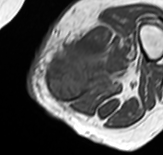
MRI of an extremity soft-tissue mass, one axial slice; position 19 of 65 along the scan axis; MR volume resampled by the dataset authors to the PET/CT grid (not the native acquisition matrix); 3.27 mm slice thickness; 163 × 155 image matrix, field of view 159 × 151 mm. Female patient. Case-level facts recorded for this patient, not image findings: histological type: pleomorphic leiomyosarcoma; grade: high; site of the primary tumour: left thigh.
Annotated regions visible in this slice (expert contour drawn on MRI and transferred to this co-registered scan by the dataset authors):
- gross tumour volume including surrounding oedema: bounding box <46,28,132,102> (left, top, right, bottom; pixels)
- gross tumour volume (mass): <46,53,102,102>